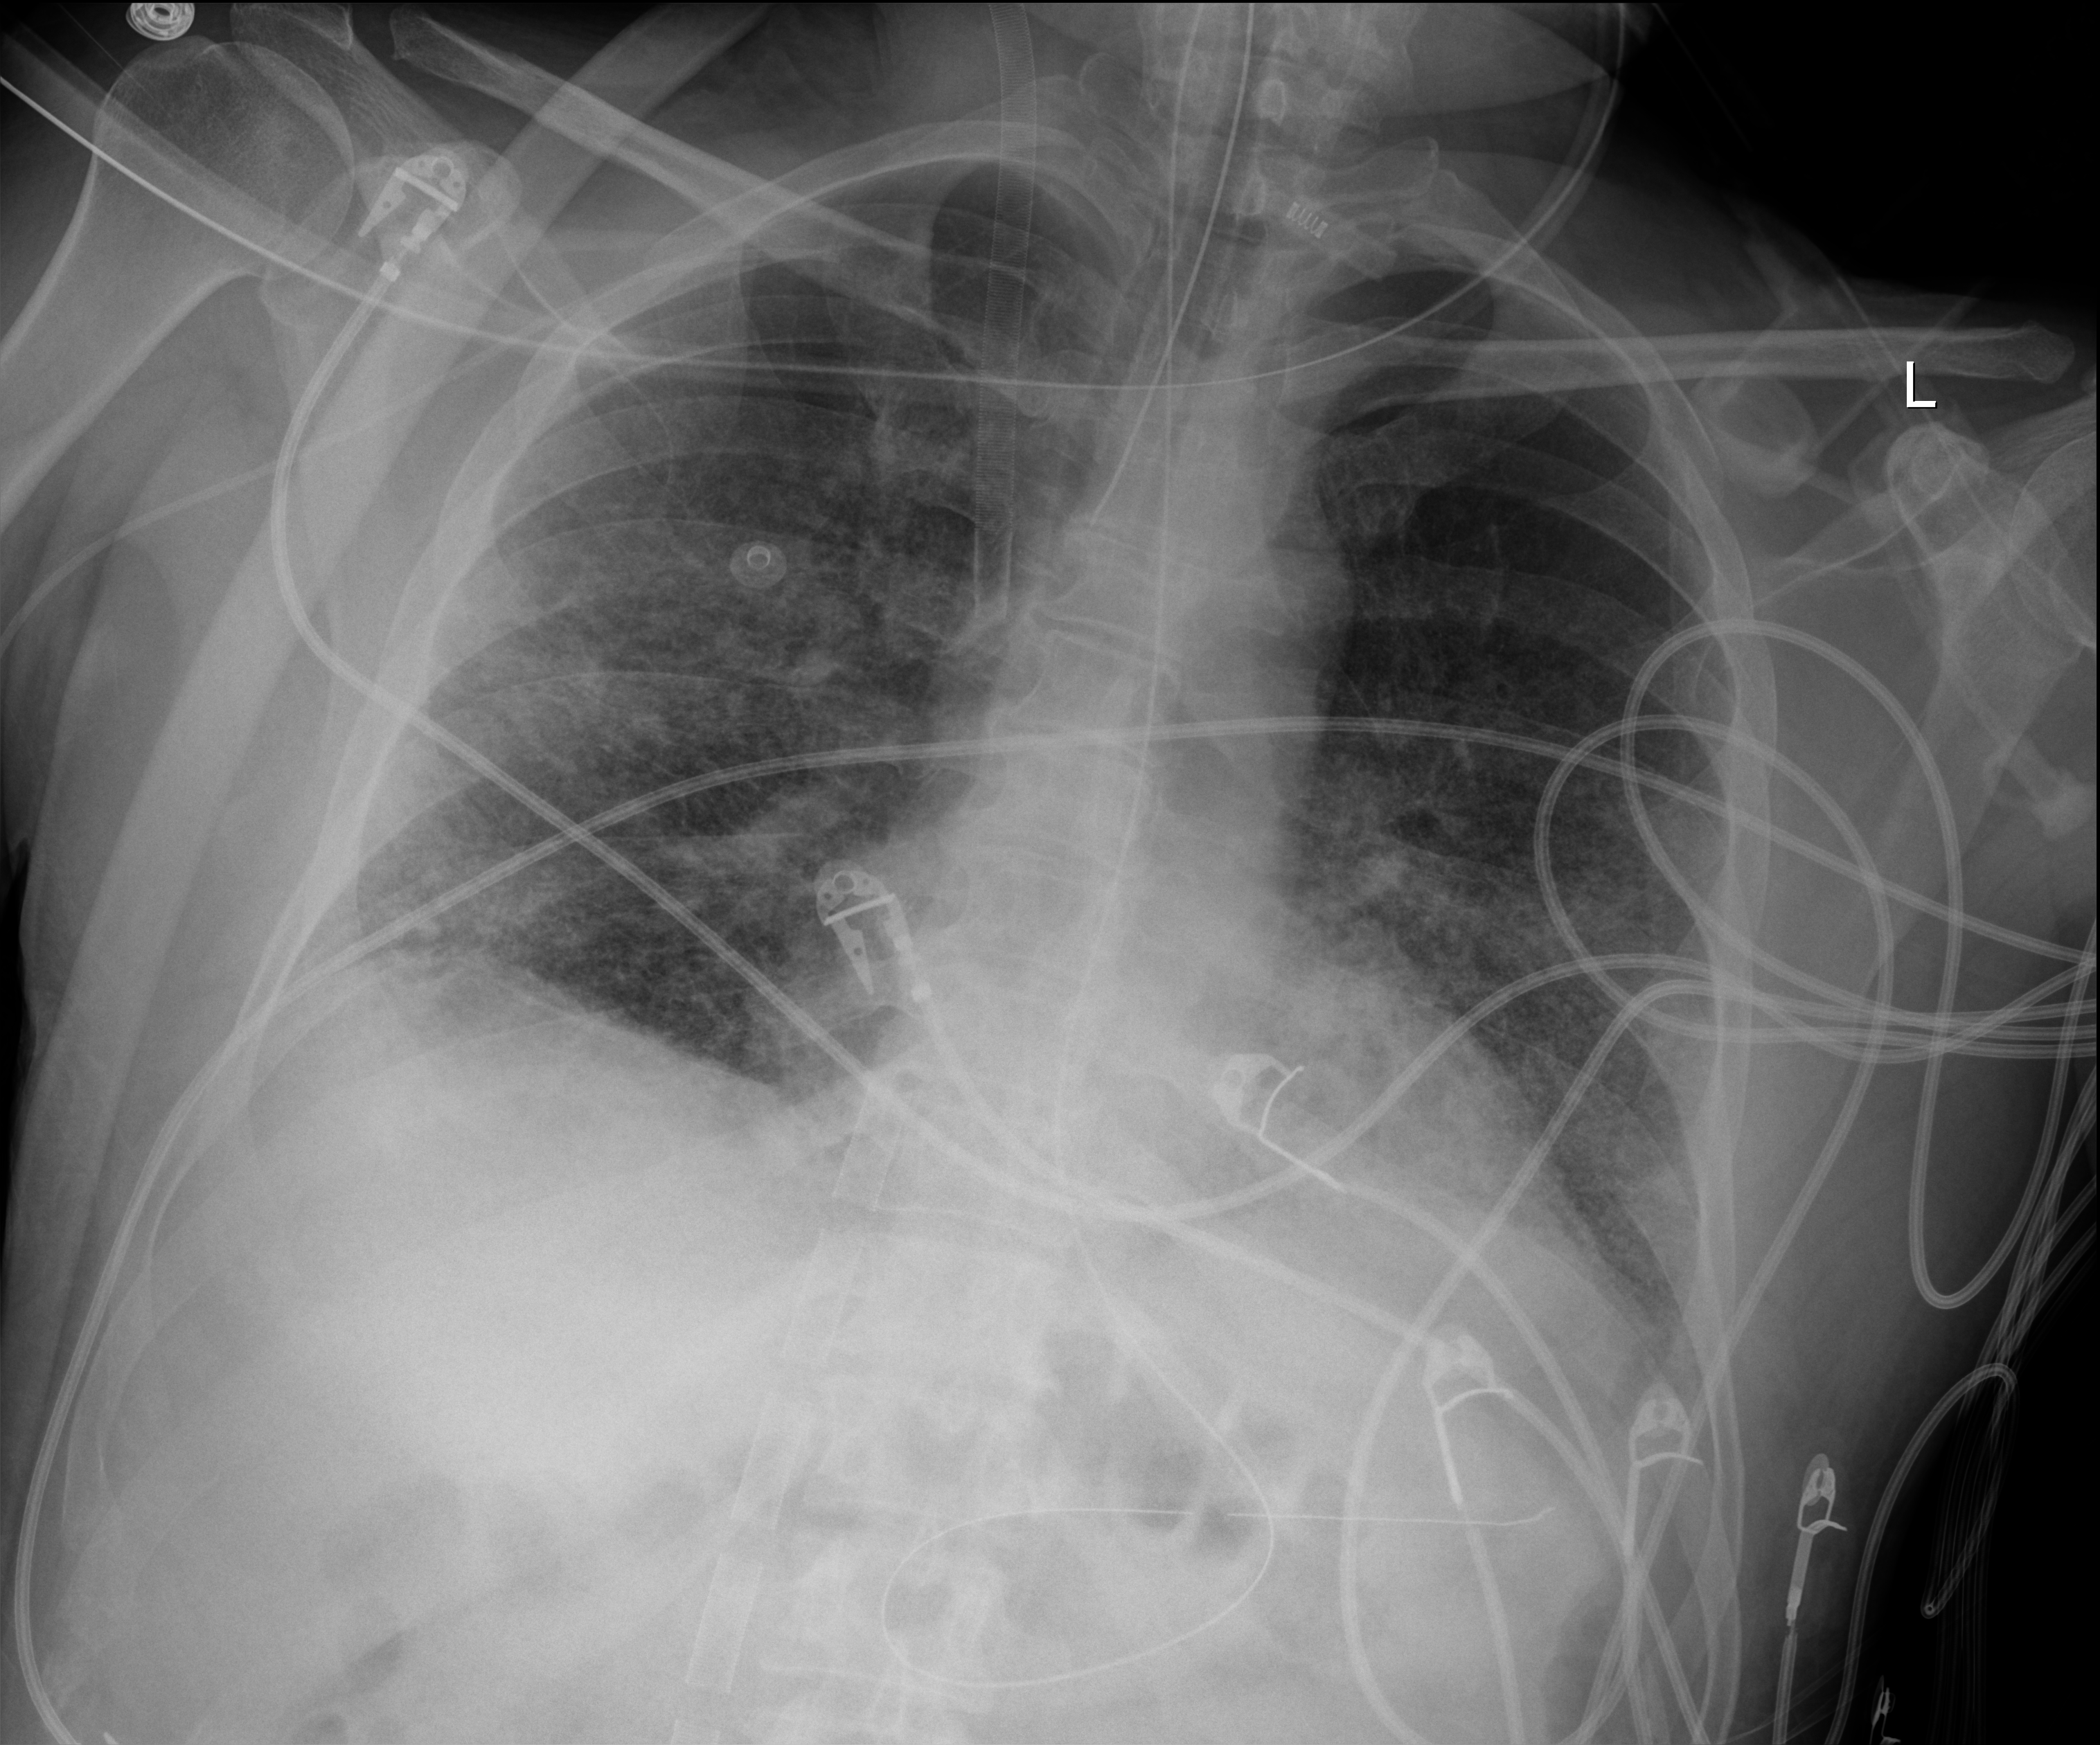
Bedside chest radiograph (digital radiography), anteroposterior (AP) projection. Male patient hospitalised with COVID-19, age 18–59 years.
Hospital-stay facts (about this admission, not read from this image; timing relative to this image not recorded): smoking status (admission record): never.